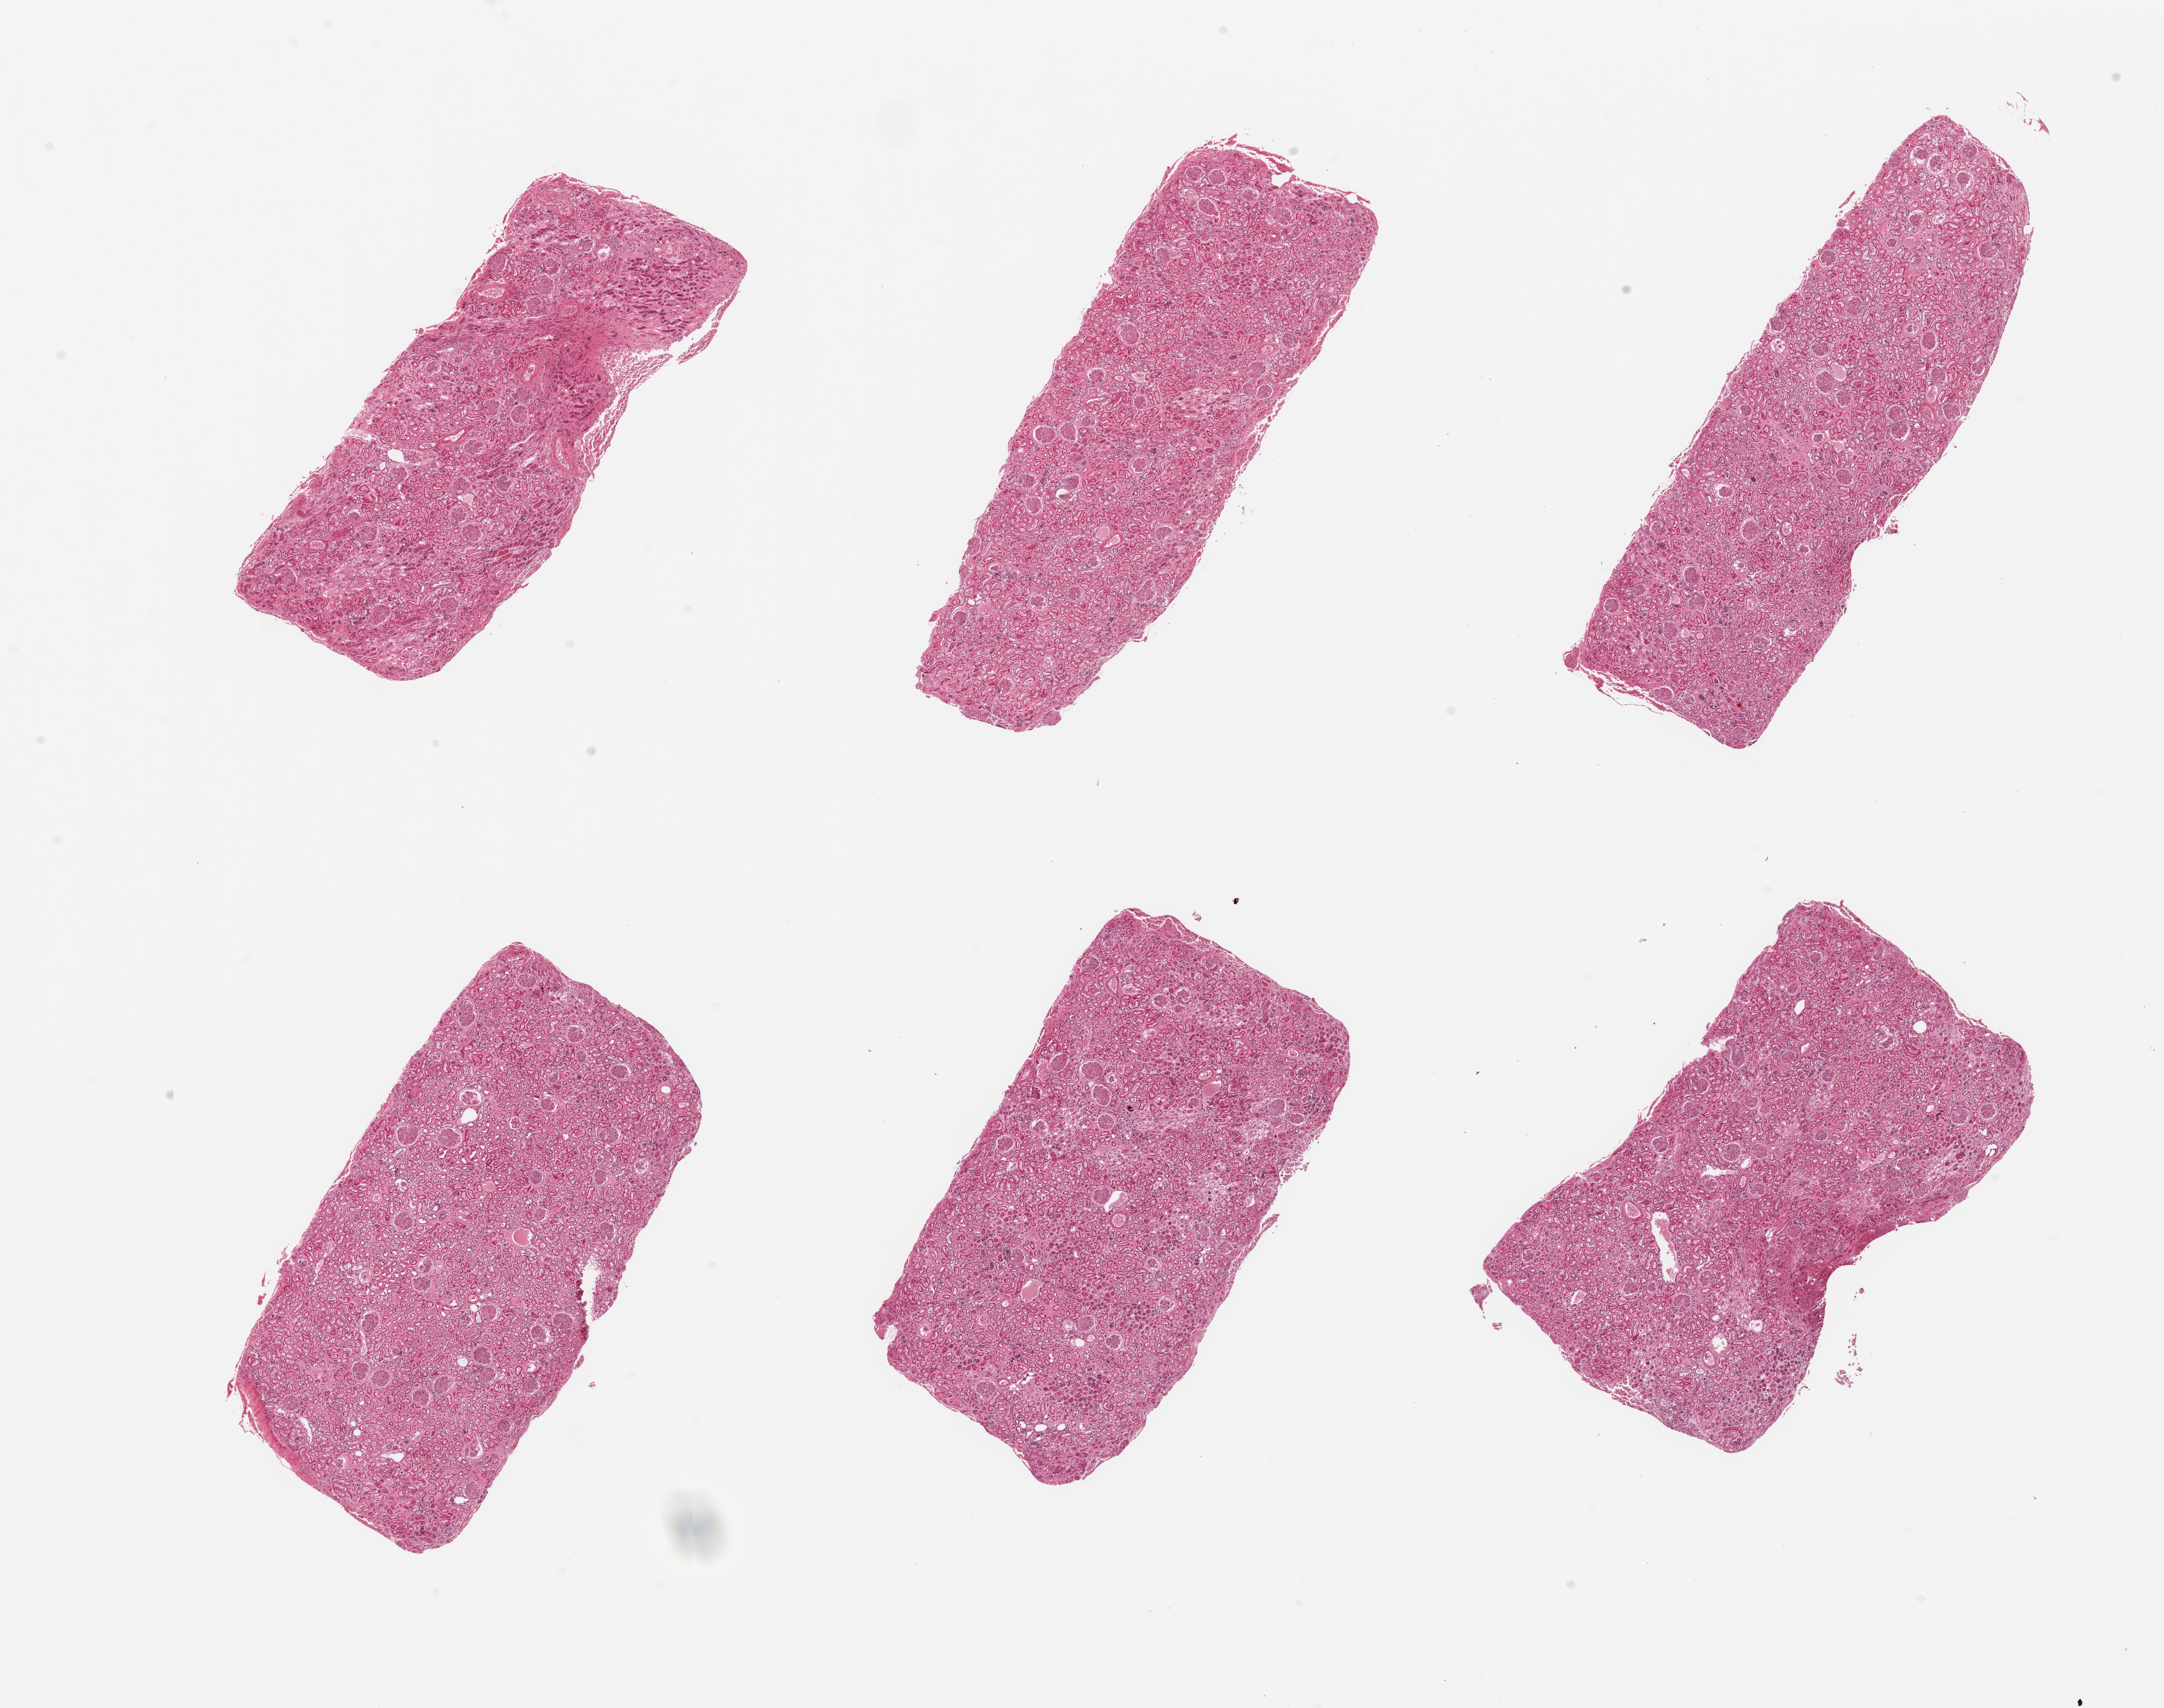
H&E whole-slide image — shown as a low-resolution overview of the whole scanned area (about 24.6 x 19.4 mm), PAXgene-fixed paraffin-embedded (PFPE) section, sampled site (target tissue): renal cortex, tissue donor sample. Donor sex: female.
* reviewer comment on this tissue sample: 6 pieces, glomeruli presrent, tubules moderately - severely autolyzied